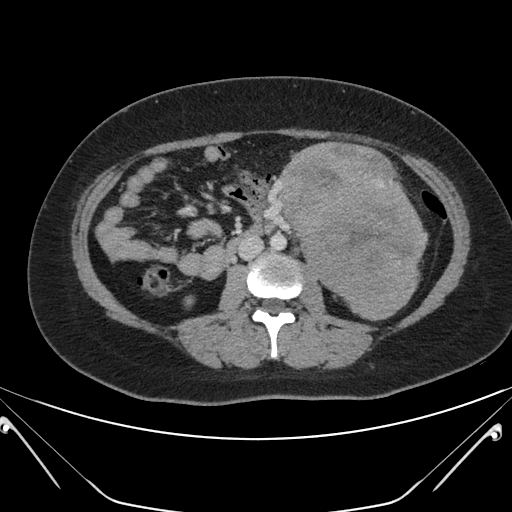
Contrast-enhanced abdominal CT, one axial slice. Slice 97 of 168 in the series (ordered by position). 120 kVp. Intravenous contrast given. Soft-tissue window (W 400 / L 40 HU). 512 × 512 image matrix, field of view 394 × 394 mm. Patient: female, 26 years. Case-level facts recorded for this patient, not image findings: diagnosis: adrenocortical carcinoma; tumour side: left adrenal; tumour size at pathology: 28 cm; Ki-67 index: 20 %; stage (as recorded): 2.
Outlined on this slice (semi-automatic segmentation, software-assisted and operator-edited):
- mass: bounding box [x1, y1, x2, y2] px = [283, 145, 423, 316]